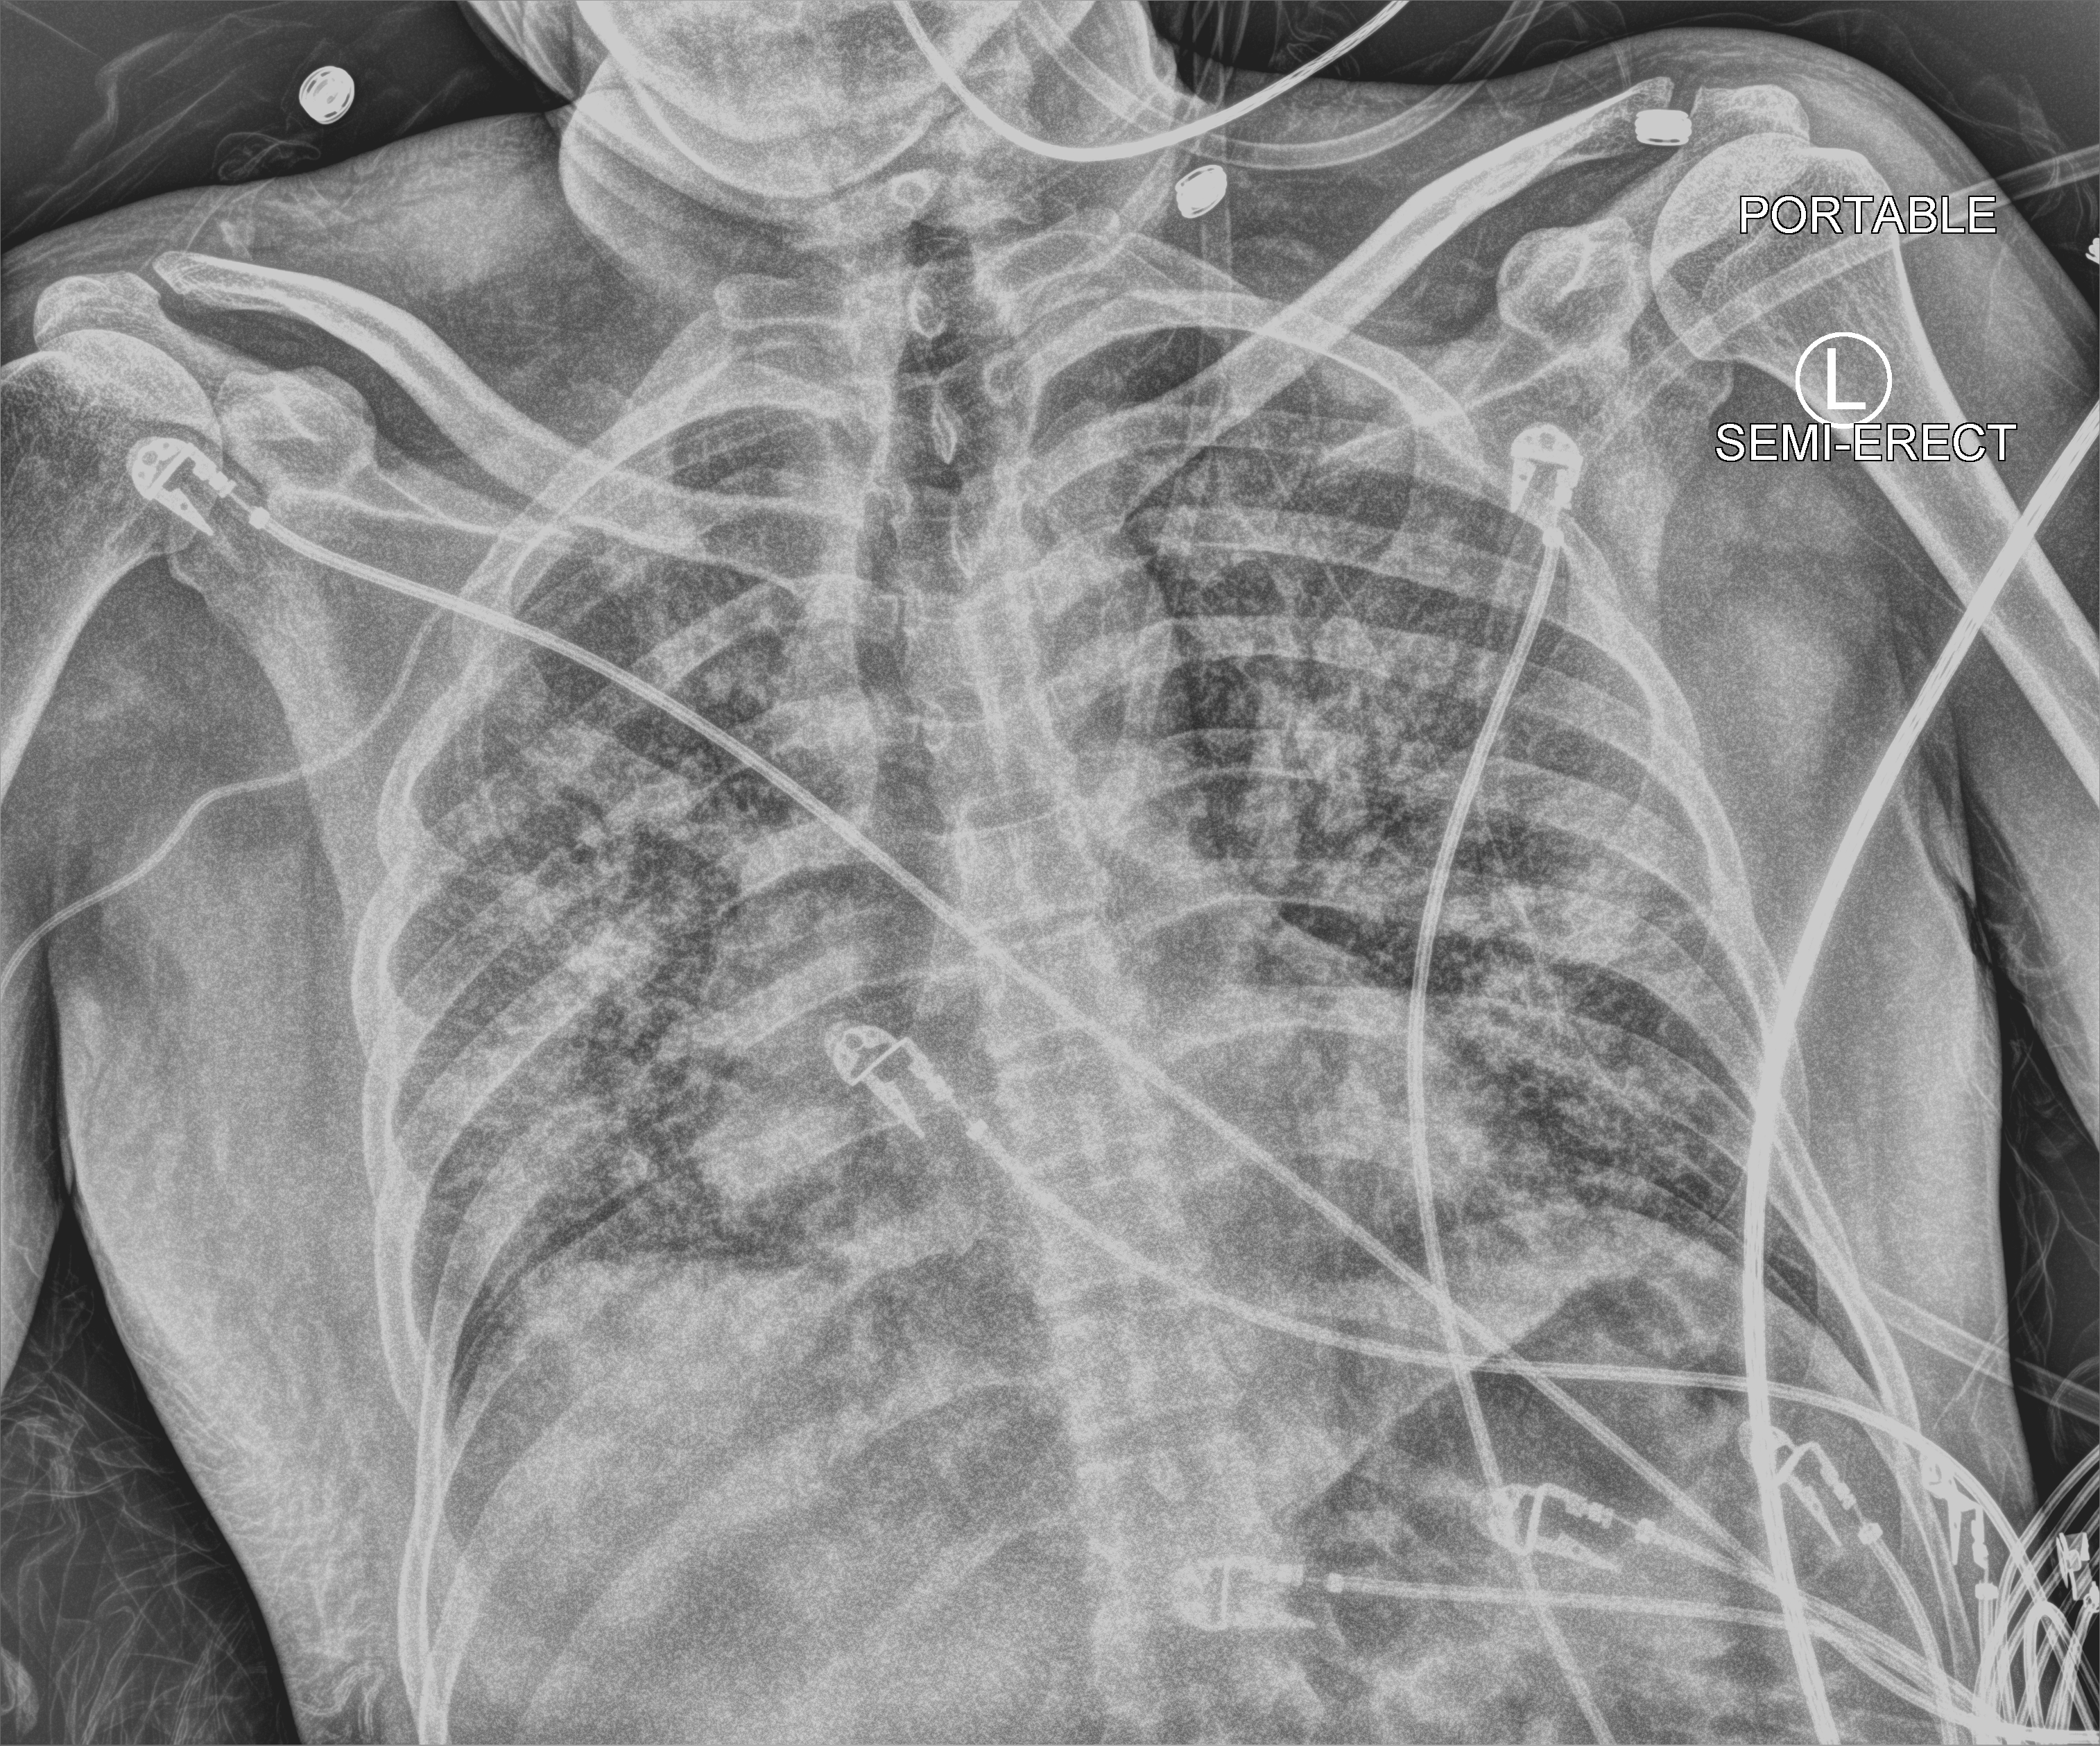
Bedside chest radiograph (computed radiography). Patient hospitalised with COVID-19, aged 18–59 years.
Hospital-stay facts (about this admission, not read from this image; timing relative to this image not recorded): admitted to intensive care during this hospital stay: yes; mechanically ventilated during this hospital stay: yes; COPD (admission record): no.